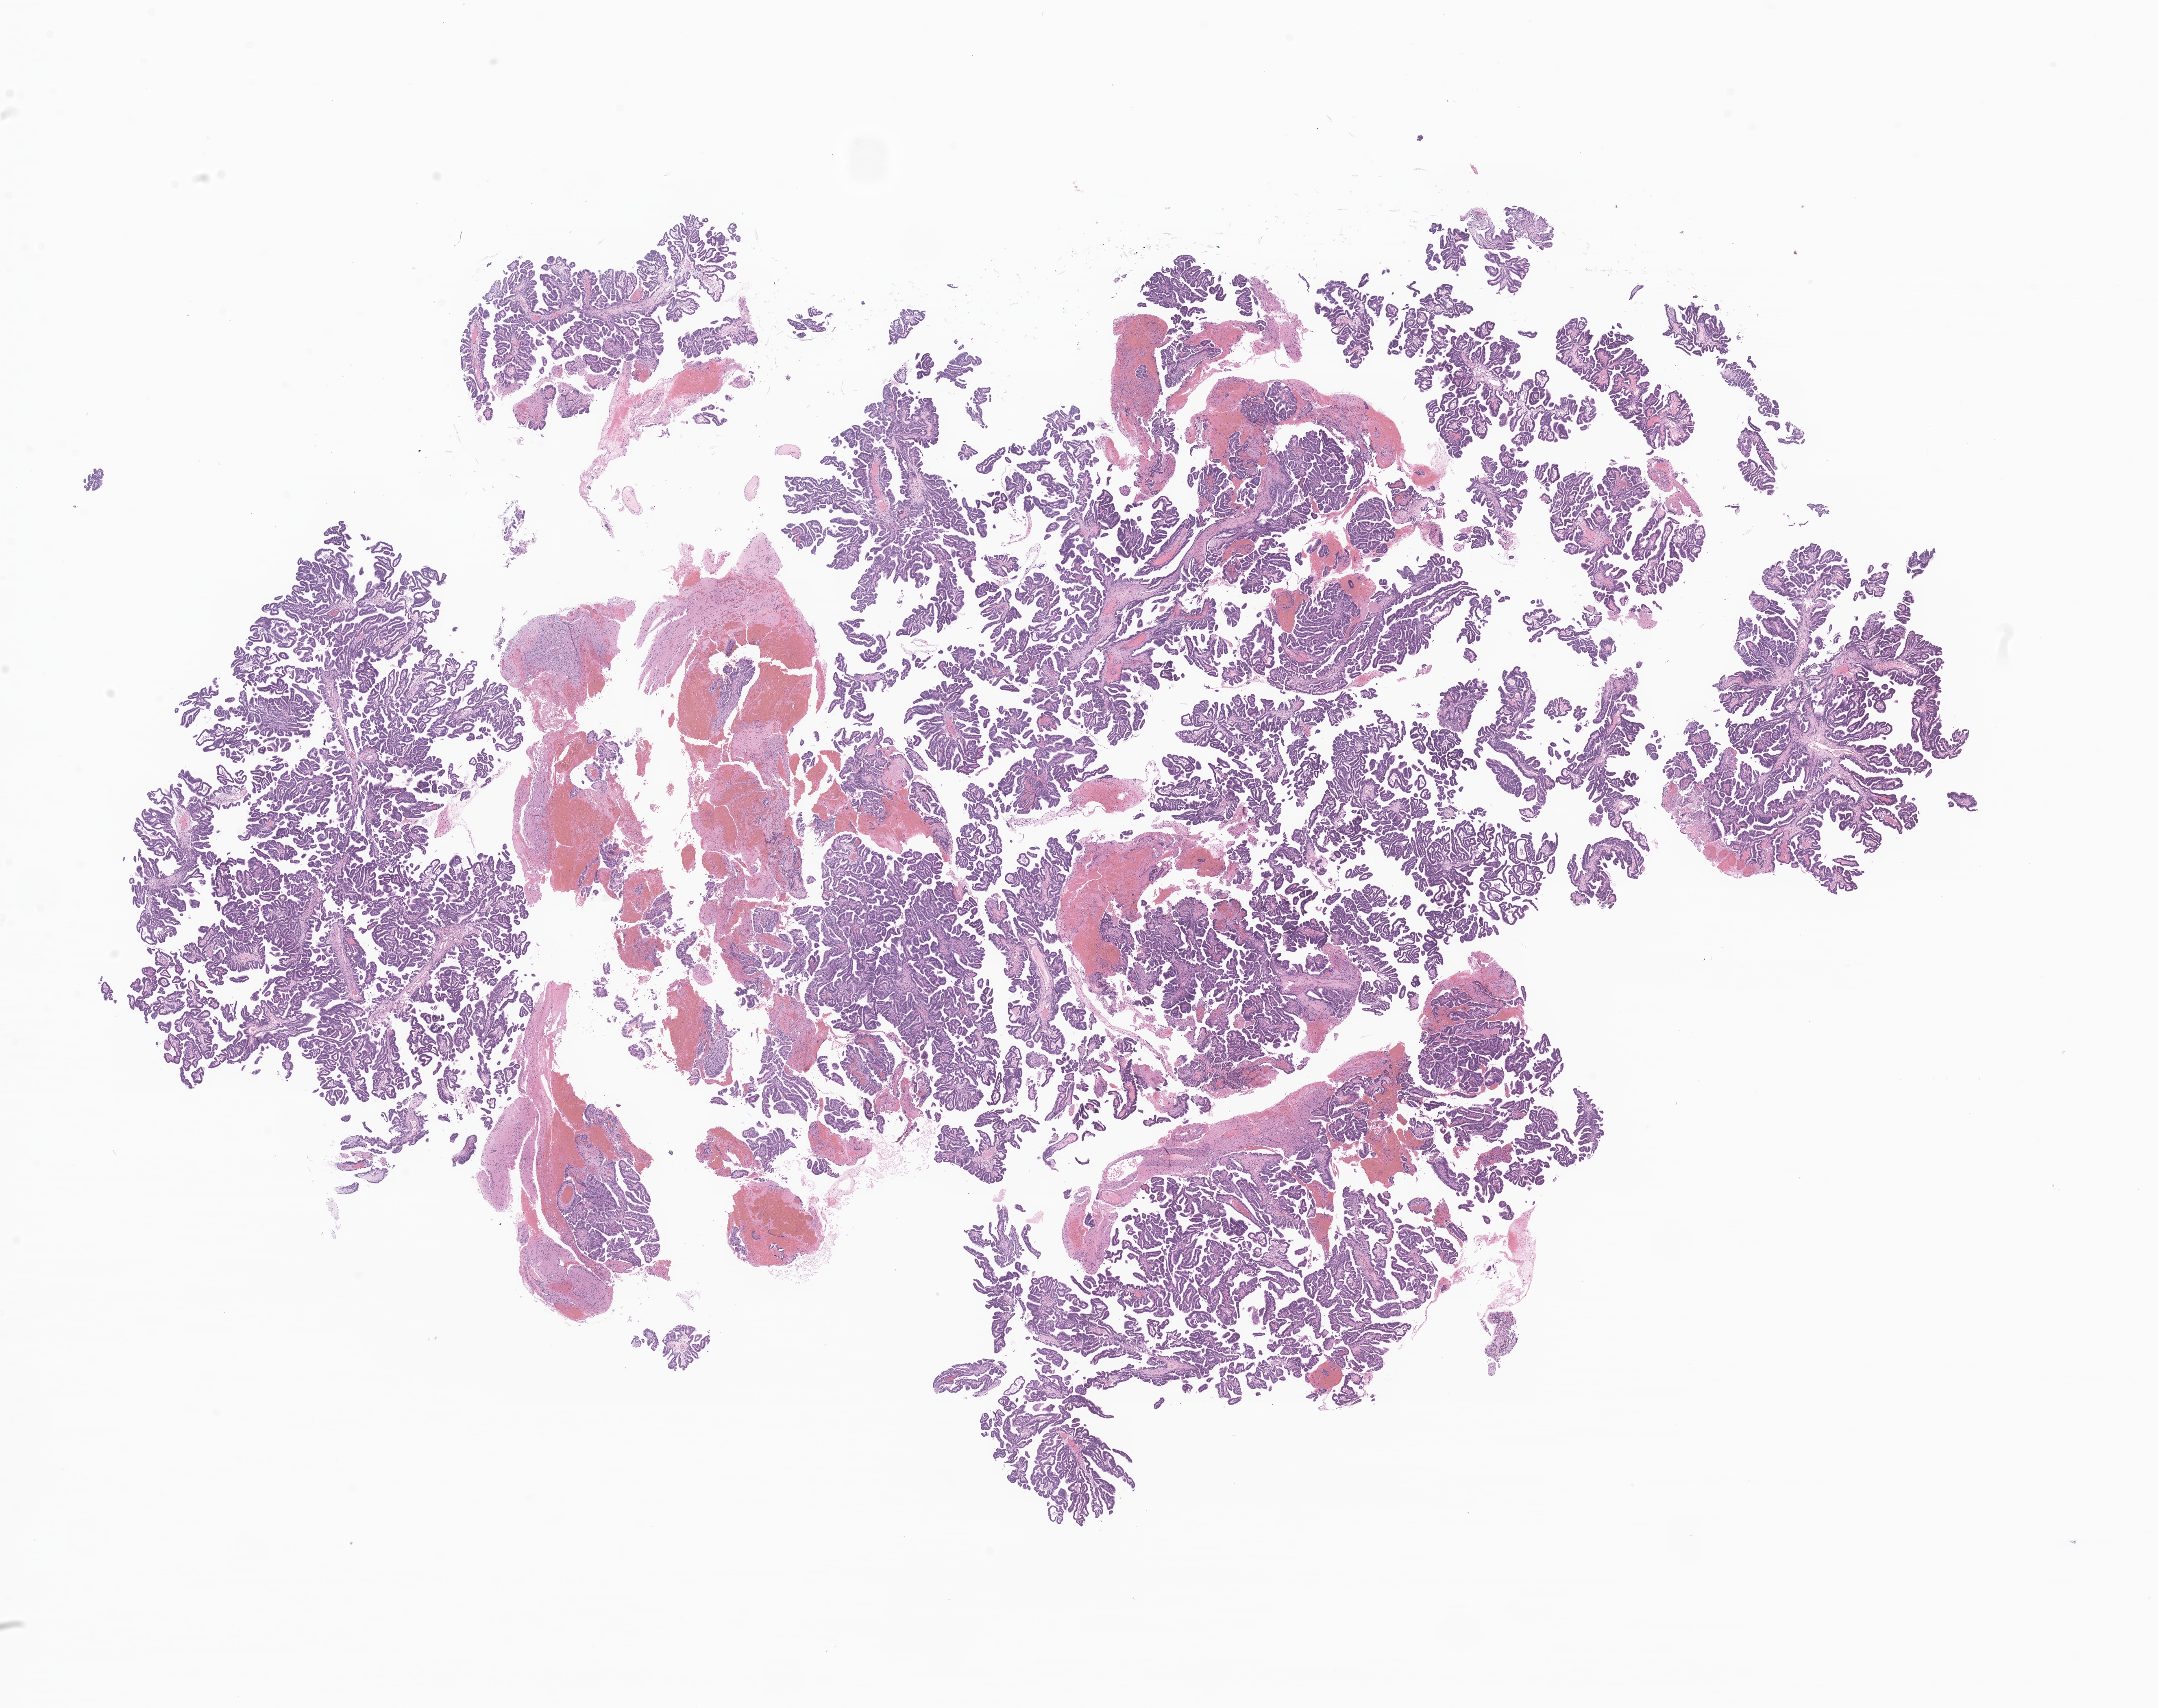
Digitized haematoxylin and eosin-stained section of tumor tissue from the cerebral ventricle, low-resolution overview of the scanned area, about 22.4 x 17.7 mm; formalin-fixed, paraffin-embedded (FFPE) tissue. Patient: male, age 295 days.
Recorded diagnosis: Choroid plexus papilloma, NOS.